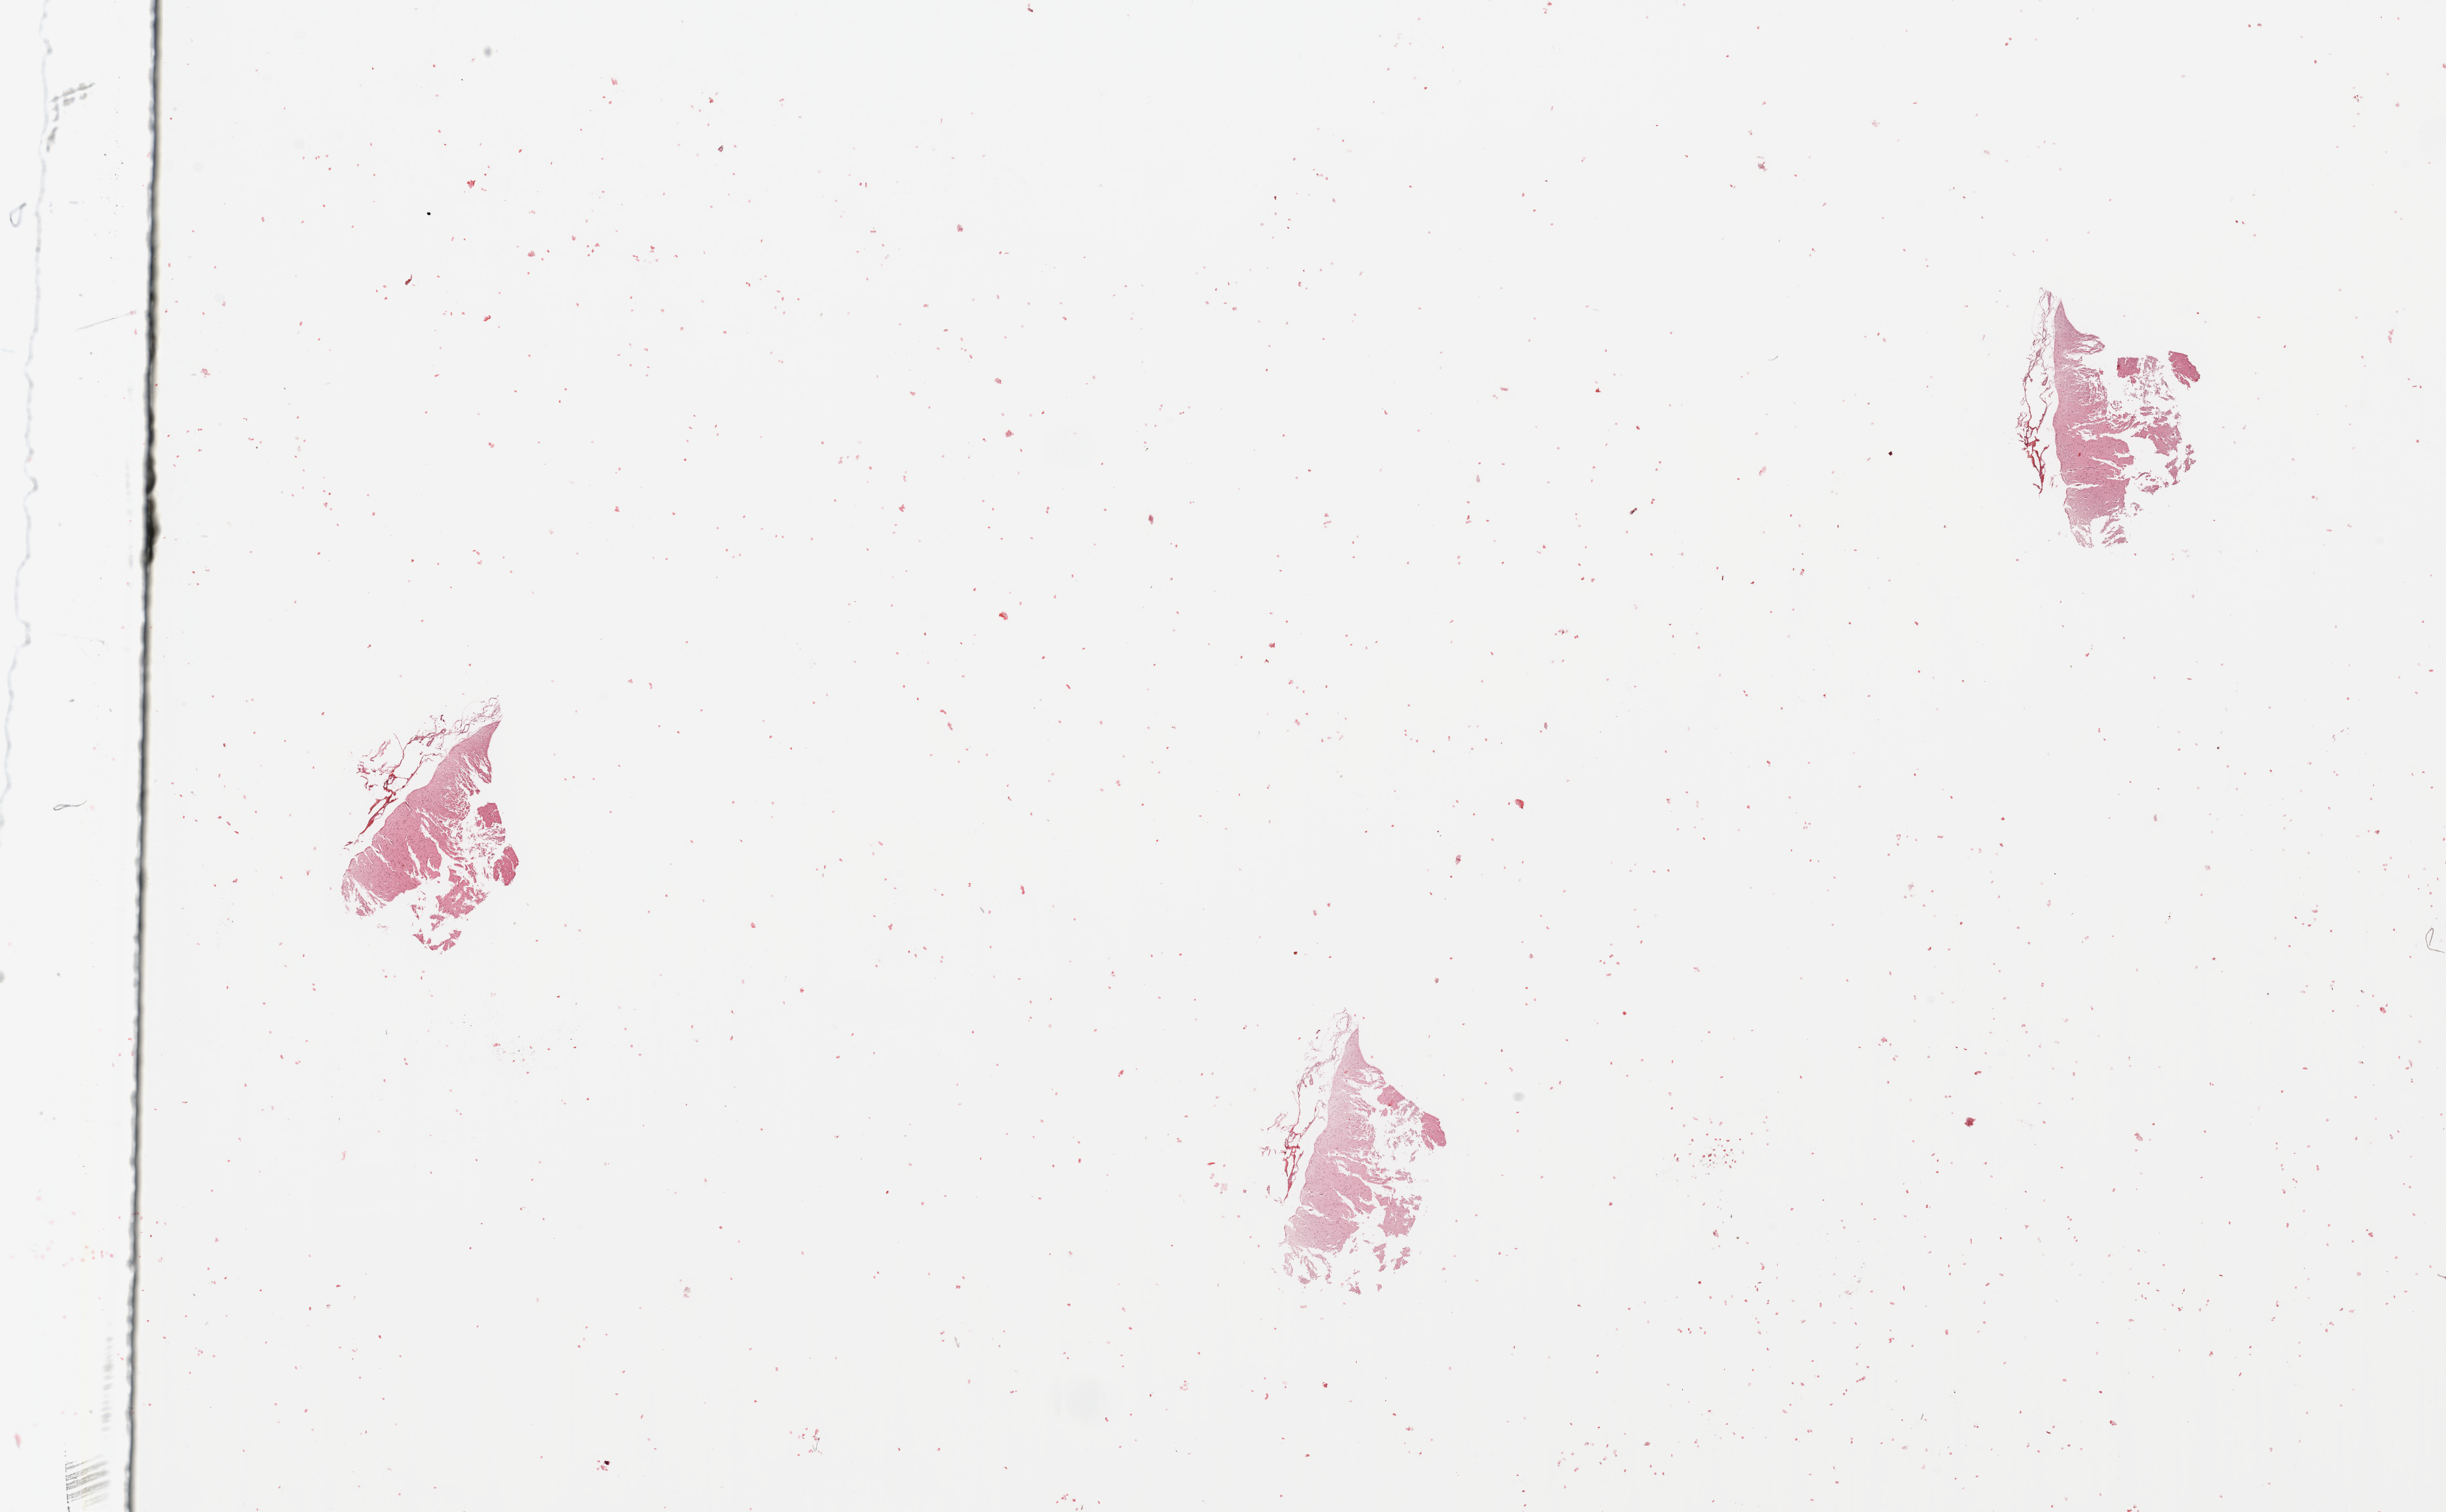
Whole-slide histology image, Hematoxylin and eosin (H&E) stained, low-resolution overview of the scanned area, about 29.5 x 18.3 mm (acquisition: 20x scan), brain, tumour tissue. 62-year-old male patient.
Primary tumour site (as recorded): frontal lobe. Histologic diagnosis: Glioblastoma.